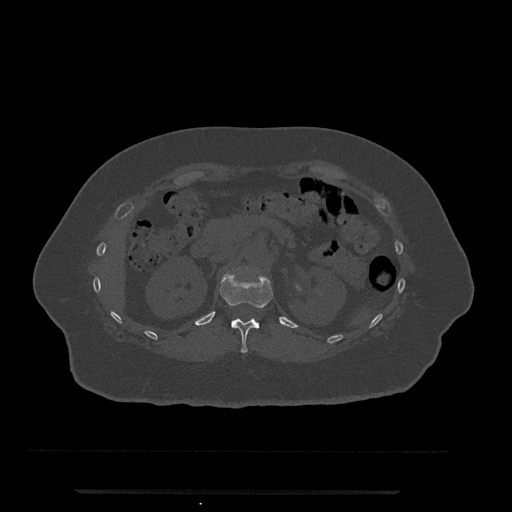
CT including the spine, one axial slice; slice 156 of 797 in the series (ordered by position); reconstruction kernel Br40s/3; bone window (W 1800 / L 400 HU); 0.5 mm slice thickness; 512 × 512 image matrix. Patient: female, 51 years. From the clinical record (not read from this slice): primary cancer: neuro.
Outlined on this slice (semi-automatically segmented with operator editing):
- T12 vertebra: box from (x=219, y=270) to (x=273, y=353) px